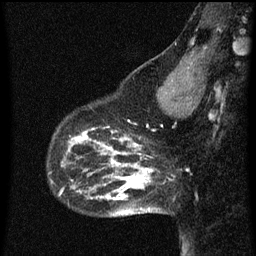
Breast MRI (dynamic contrast-enhanced), one sagittal slice; slice 17 of 60 in the series (ordered by position); dynamic contrast-enhanced series, image 2 of 3 at this slice position (ordered by acquisition); 1.5 T; TE 4.2 ms, TR 8 ms; 256 × 256 image matrix, field of view 180 × 180 mm. Patient: female, 43 years.
Outlined on this slice (semi-automatic segmentation, software-assisted and operator-edited):
- analysis volume of interest (the breast-tissue region the enhancement analysis was run in; not a lesion): box from (x=53, y=106) to (x=101, y=155) px
- tumour enhancement mask (voxels above the 70 % enhancement threshold inside the analysis volume of interest): (x=68, y=128)–(x=101, y=153)